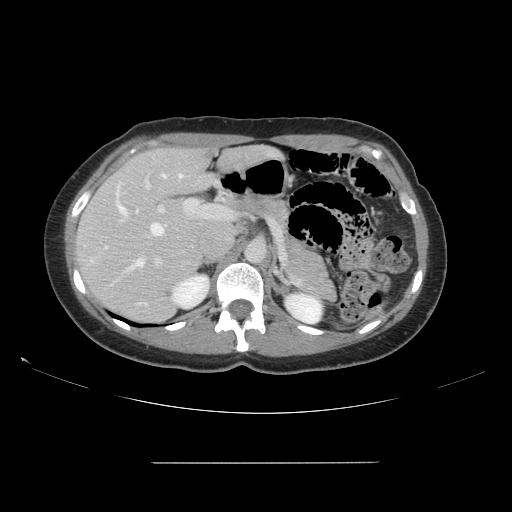
Contrast-enhanced abdominal CT, one axial slice. Slice 98 of 151 in the series (ordered by position). Intravenous contrast given. Soft-tissue window (W 400 / L 40 HU). 2.5 mm slice thickness. 512 × 512 image matrix, field of view 421 × 421 mm. Female patient, age 46 years. Case-level facts recorded for this patient, not image findings: diagnosis: colorectal cancer liver metastases, imaged before liver resection; multiple liver metastases: yes; largest metastasis: 3 cm; disease in both lobes: yes.
Outlined on this slice (outlined manually by an expert reader):
- hepatic veins: bounding box [x1, y1, x2, y2] px = [115, 174, 183, 271]
- liver: [76, 148, 220, 323]
- planned liver remnant (the part of the liver to remain after resection): [89, 150, 214, 257]
- portal vein (with intrahepatic branches): [118, 178, 232, 266]